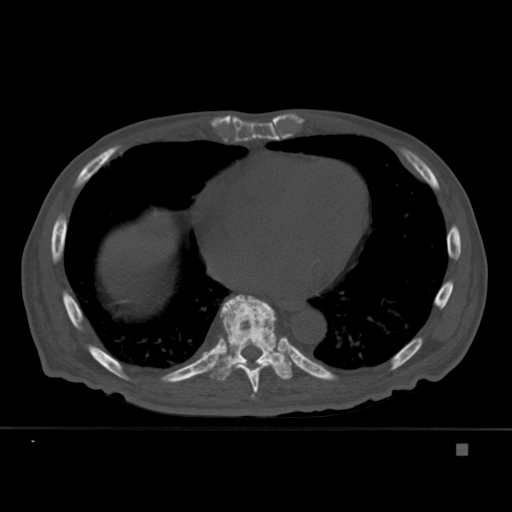
CT including the spine, one axial slice; slice 254 of 451 in the series (ordered by position); bone window (W 1800 / L 400 HU); 512 × 512 image matrix. Patient: male, 75 years. From the clinical record (not read from this slice): primary cancer: prostate.
Structures marked on this image (semi-automatic segmentation, software-assisted and operator-edited):
- T7 vertebra: bounding box (x1, y1, x2, y2) in pixels: (251, 394, 255, 400)
- T8 vertebra: (227, 337, 270, 394)
- T9 vertebra: (206, 295, 296, 381)